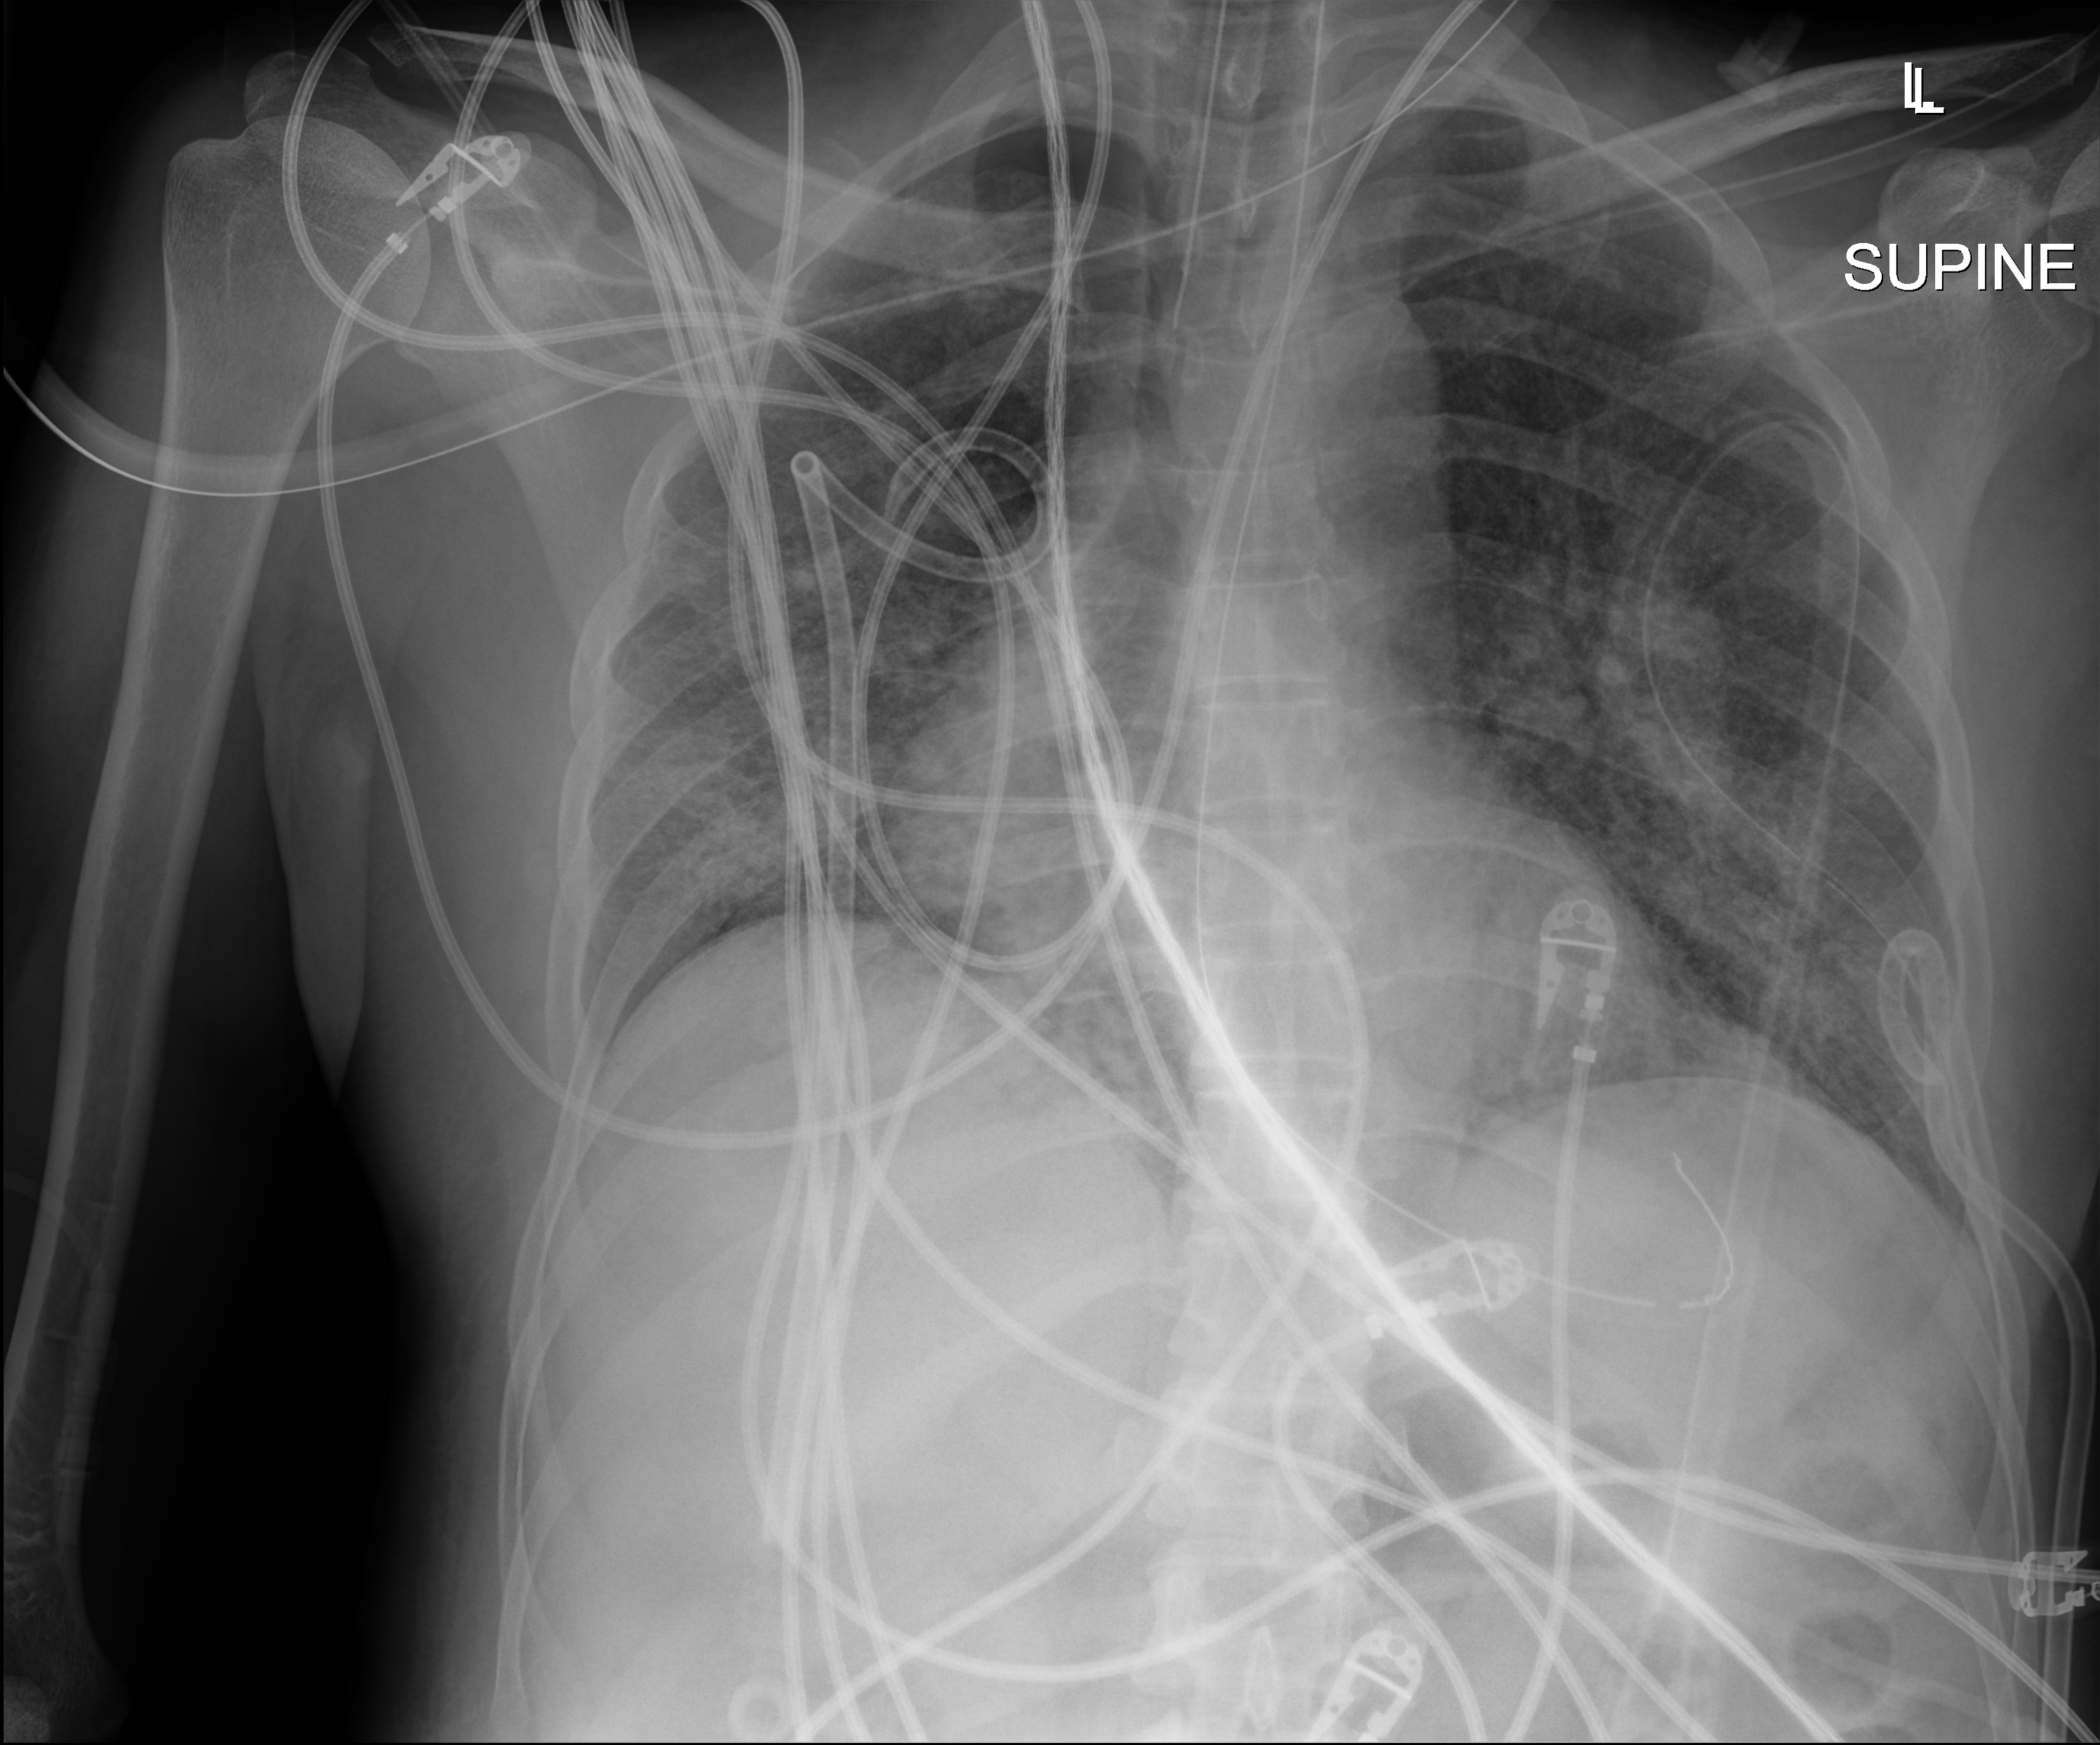
Chest X-ray (portable), anteroposterior (AP) projection. Patient hospitalised with COVID-19, aged 18–59 years.
Admission-level facts for this patient (not findings on this image; timing relative to this image not recorded): mechanically ventilated during this hospital stay: yes; admitted to intensive care during this hospital stay: yes.